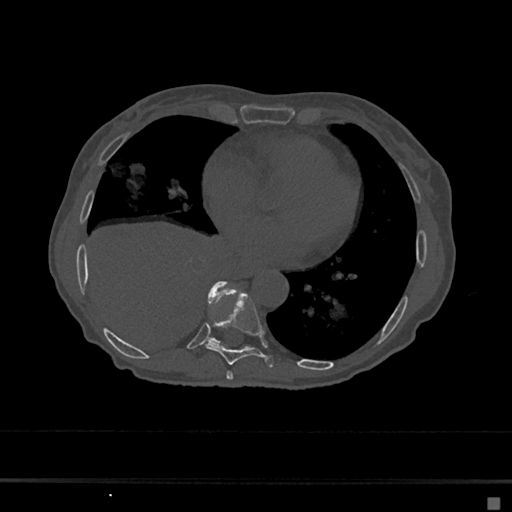
CT including the spine, one axial slice; position 311 of 797 along the scan axis; 120 kVp; bone window (W 1800 / L 400 HU); 0.5 mm slice thickness; 512 × 512 image matrix, field of view 360 × 360 mm. Female patient, age 68 years. From the clinical record (not read from this slice): primary cancer: renal.
Outlined on this slice (semi-automatic segmentation, software-assisted and operator-edited):
- T7 vertebra: bounding box (x1, y1, x2, y2) in pixels: (226, 371, 233, 380)
- T8 vertebra: (205, 291, 274, 367)
- T9 vertebra: (208, 281, 226, 345)